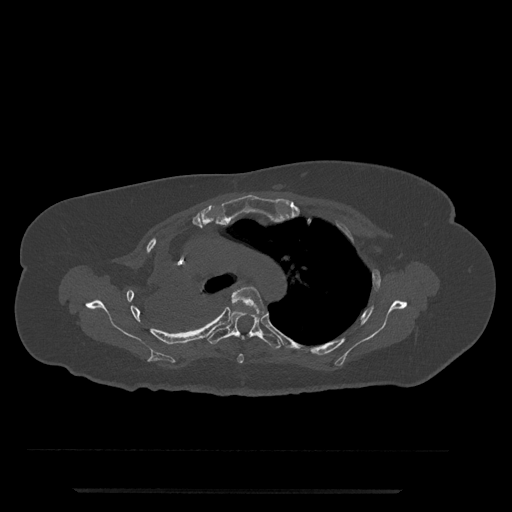
CT including the spine, one axial slice. Position 561 of 797 along the scan axis. Reconstruction kernel Br40s/3. 120 kVp. Bone window (W 1800 / L 400 HU). 0.5 mm slice thickness. 512 × 512 image matrix, field of view 440 × 440 mm. Patient: female, 51 years. Case-level facts recorded for this patient, not image findings: primary cancer: neuro; vertebrae with lytic lesions (as recorded): T8.
Structures marked on this image (semi-automatically segmented with operator editing):
- T4 vertebra: bounding box <231,286,264,363> (left, top, right, bottom; pixels)
- T5 vertebra: <206,308,282,349>